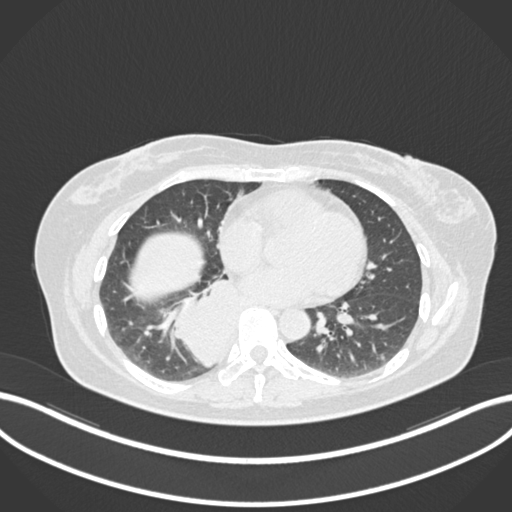
Chest CT, one axial slice. Slice 565 of 677 in the series (ordered by position). Lung window (W 1500 / L -600 HU). 512 × 512 image matrix, field of view 400 × 400 mm. Female patient, age 54 years. From the clinical record (not read from this slice): clinical TNM (as recorded): T4 N0 M0.
Annotated regions visible in this slice (rectangle marked by the reading radiologist):
- lung tumour (recorded histology: adenocarcinoma): bounding box [x1, y1, x2, y2] px = [168, 276, 241, 371]